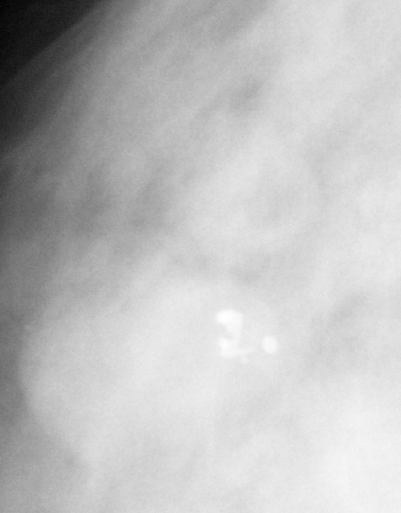
Crop from a digitized film mammogram around one marked abnormality; right breast; CC view; BI-RADS breast density category 3 (scale 1–4).
- Calcifications, morphology pleomorphic, distribution clustered; BI-RADS assessment category 4; subtlety rating 4 on a 1 (subtle) to 5 (obvious) scale; pathology result (as recorded, not read from the image): benign.